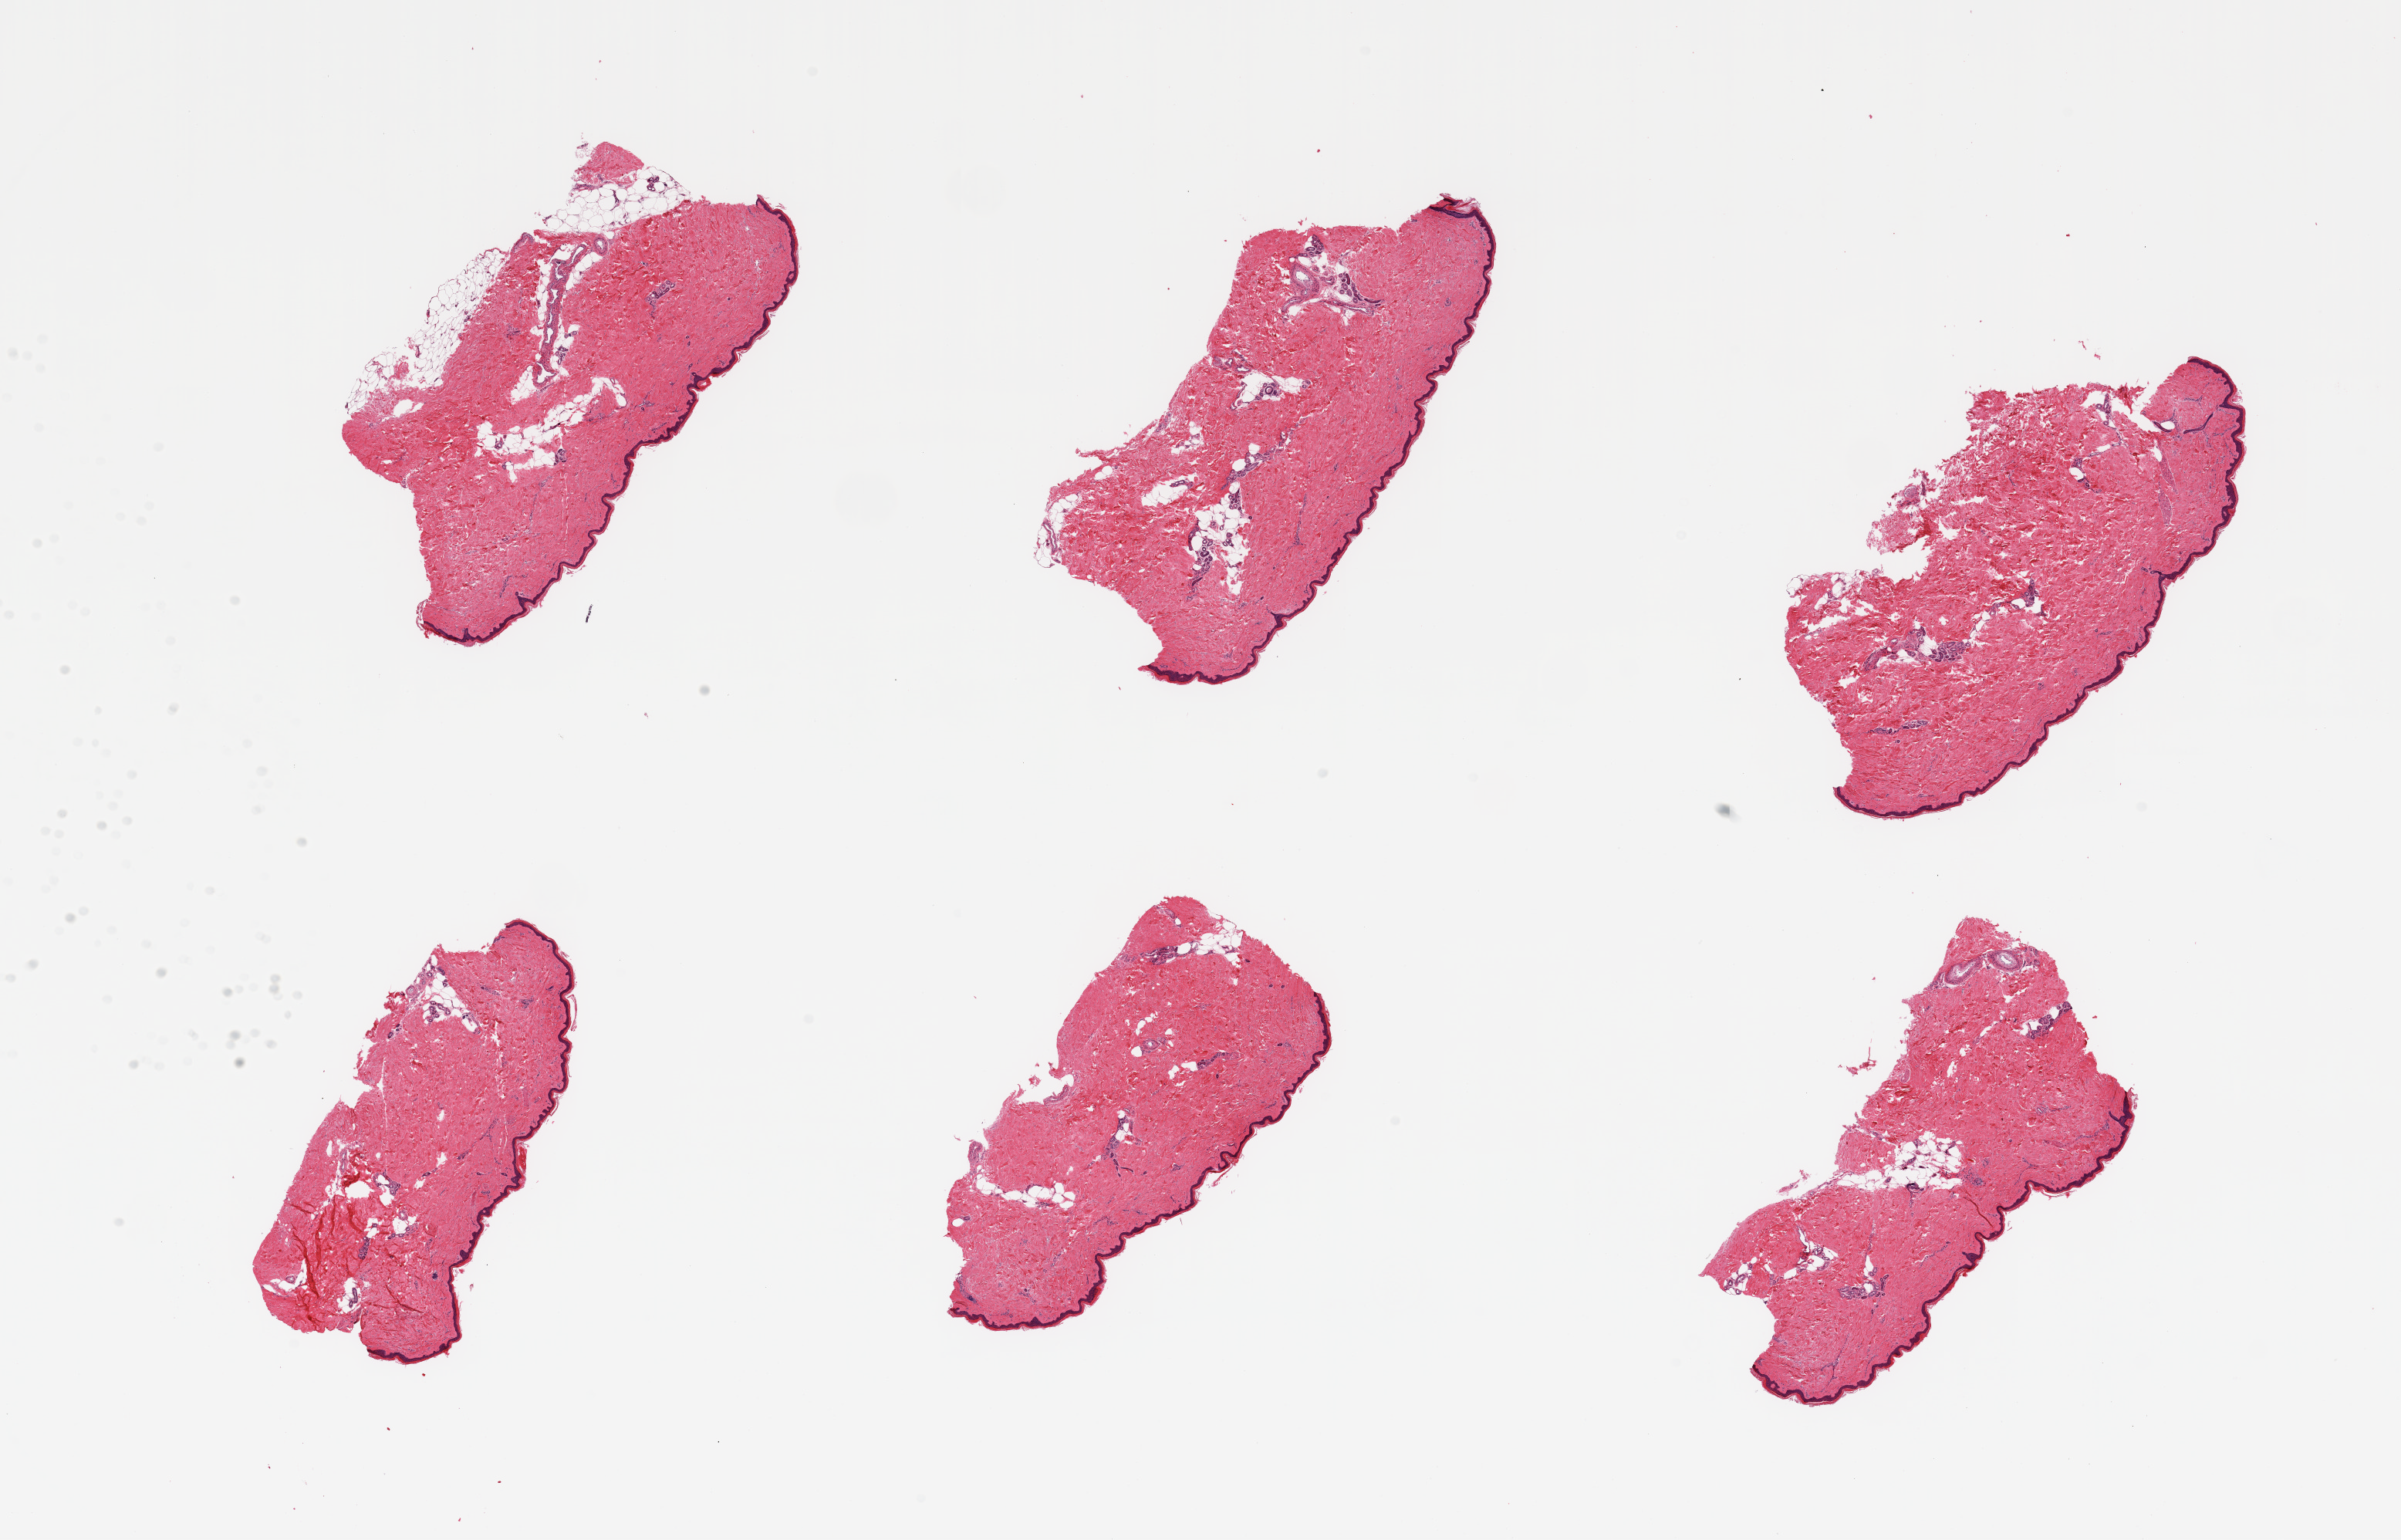
Digitized H&E-stained section, brightfield — whole scanned area (about 24.6 x 15.8 mm, acquisition: 20x scan) shown as a low-resolution overview. PAXgene-fixed, paraffin-embedded tissue. Sampled site (target tissue): skin of lower leg. Tissue donor sample. Female donor.
Pathologist's review note for this sample: 6 pieces, squamous epithelium is ~40 microns; no significant dermal fat.